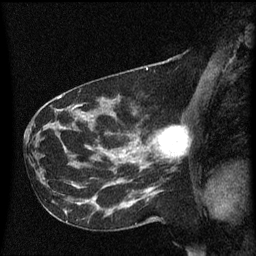
Breast MRI (dynamic contrast-enhanced), one sagittal slice. Slice 29 of 60 in the series (ordered by position). Dynamic contrast-enhanced series, image 2 of 3 at this slice position (ordered by acquisition). 1.5 T. TE 4.2 ms, TR 8.4 ms. 2 mm slice thickness. 256 × 256 image matrix, field of view 200 × 200 mm. Patient: female, 41 years. From the clinical record (not read from this slice): setting: breast cancer imaged before/during neoadjuvant chemotherapy; receptor status: triple-negative.
Structures marked on this image (semi-automatically segmented with operator editing):
- analysis volume of interest (the breast-tissue region the enhancement analysis was run in; not a lesion): bounding box [x1, y1, x2, y2] px = [138, 126, 188, 173]
- tumour enhancement mask (voxels above the 70 % enhancement threshold inside the analysis volume of interest): [154, 126, 187, 157]